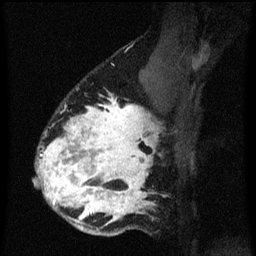
Breast MRI (dynamic contrast-enhanced), one sagittal slice; slice 44 of 60 in the series (ordered by position); dynamic contrast-enhanced series, image 2 of 3 at this slice position (ordered by acquisition); 1.5 T; TE 4.2 ms, TR 8.4 ms; 256 × 256 image matrix, field of view 180 × 180 mm. Patient: female, 34 years. From the clinical record (not read from this slice): setting: breast cancer imaged before/during neoadjuvant chemotherapy; receptor status: HR-positive, HER2-negative.
Outlined on this slice (semi-automatic segmentation, software-assisted and operator-edited):
- analysis volume of interest (the breast-tissue region the enhancement analysis was run in; not a lesion): box from (x=34, y=58) to (x=171, y=237) px
- tumour enhancement mask (voxels above the 70 % enhancement threshold inside the analysis volume of interest): (x=38, y=98)–(x=157, y=229)